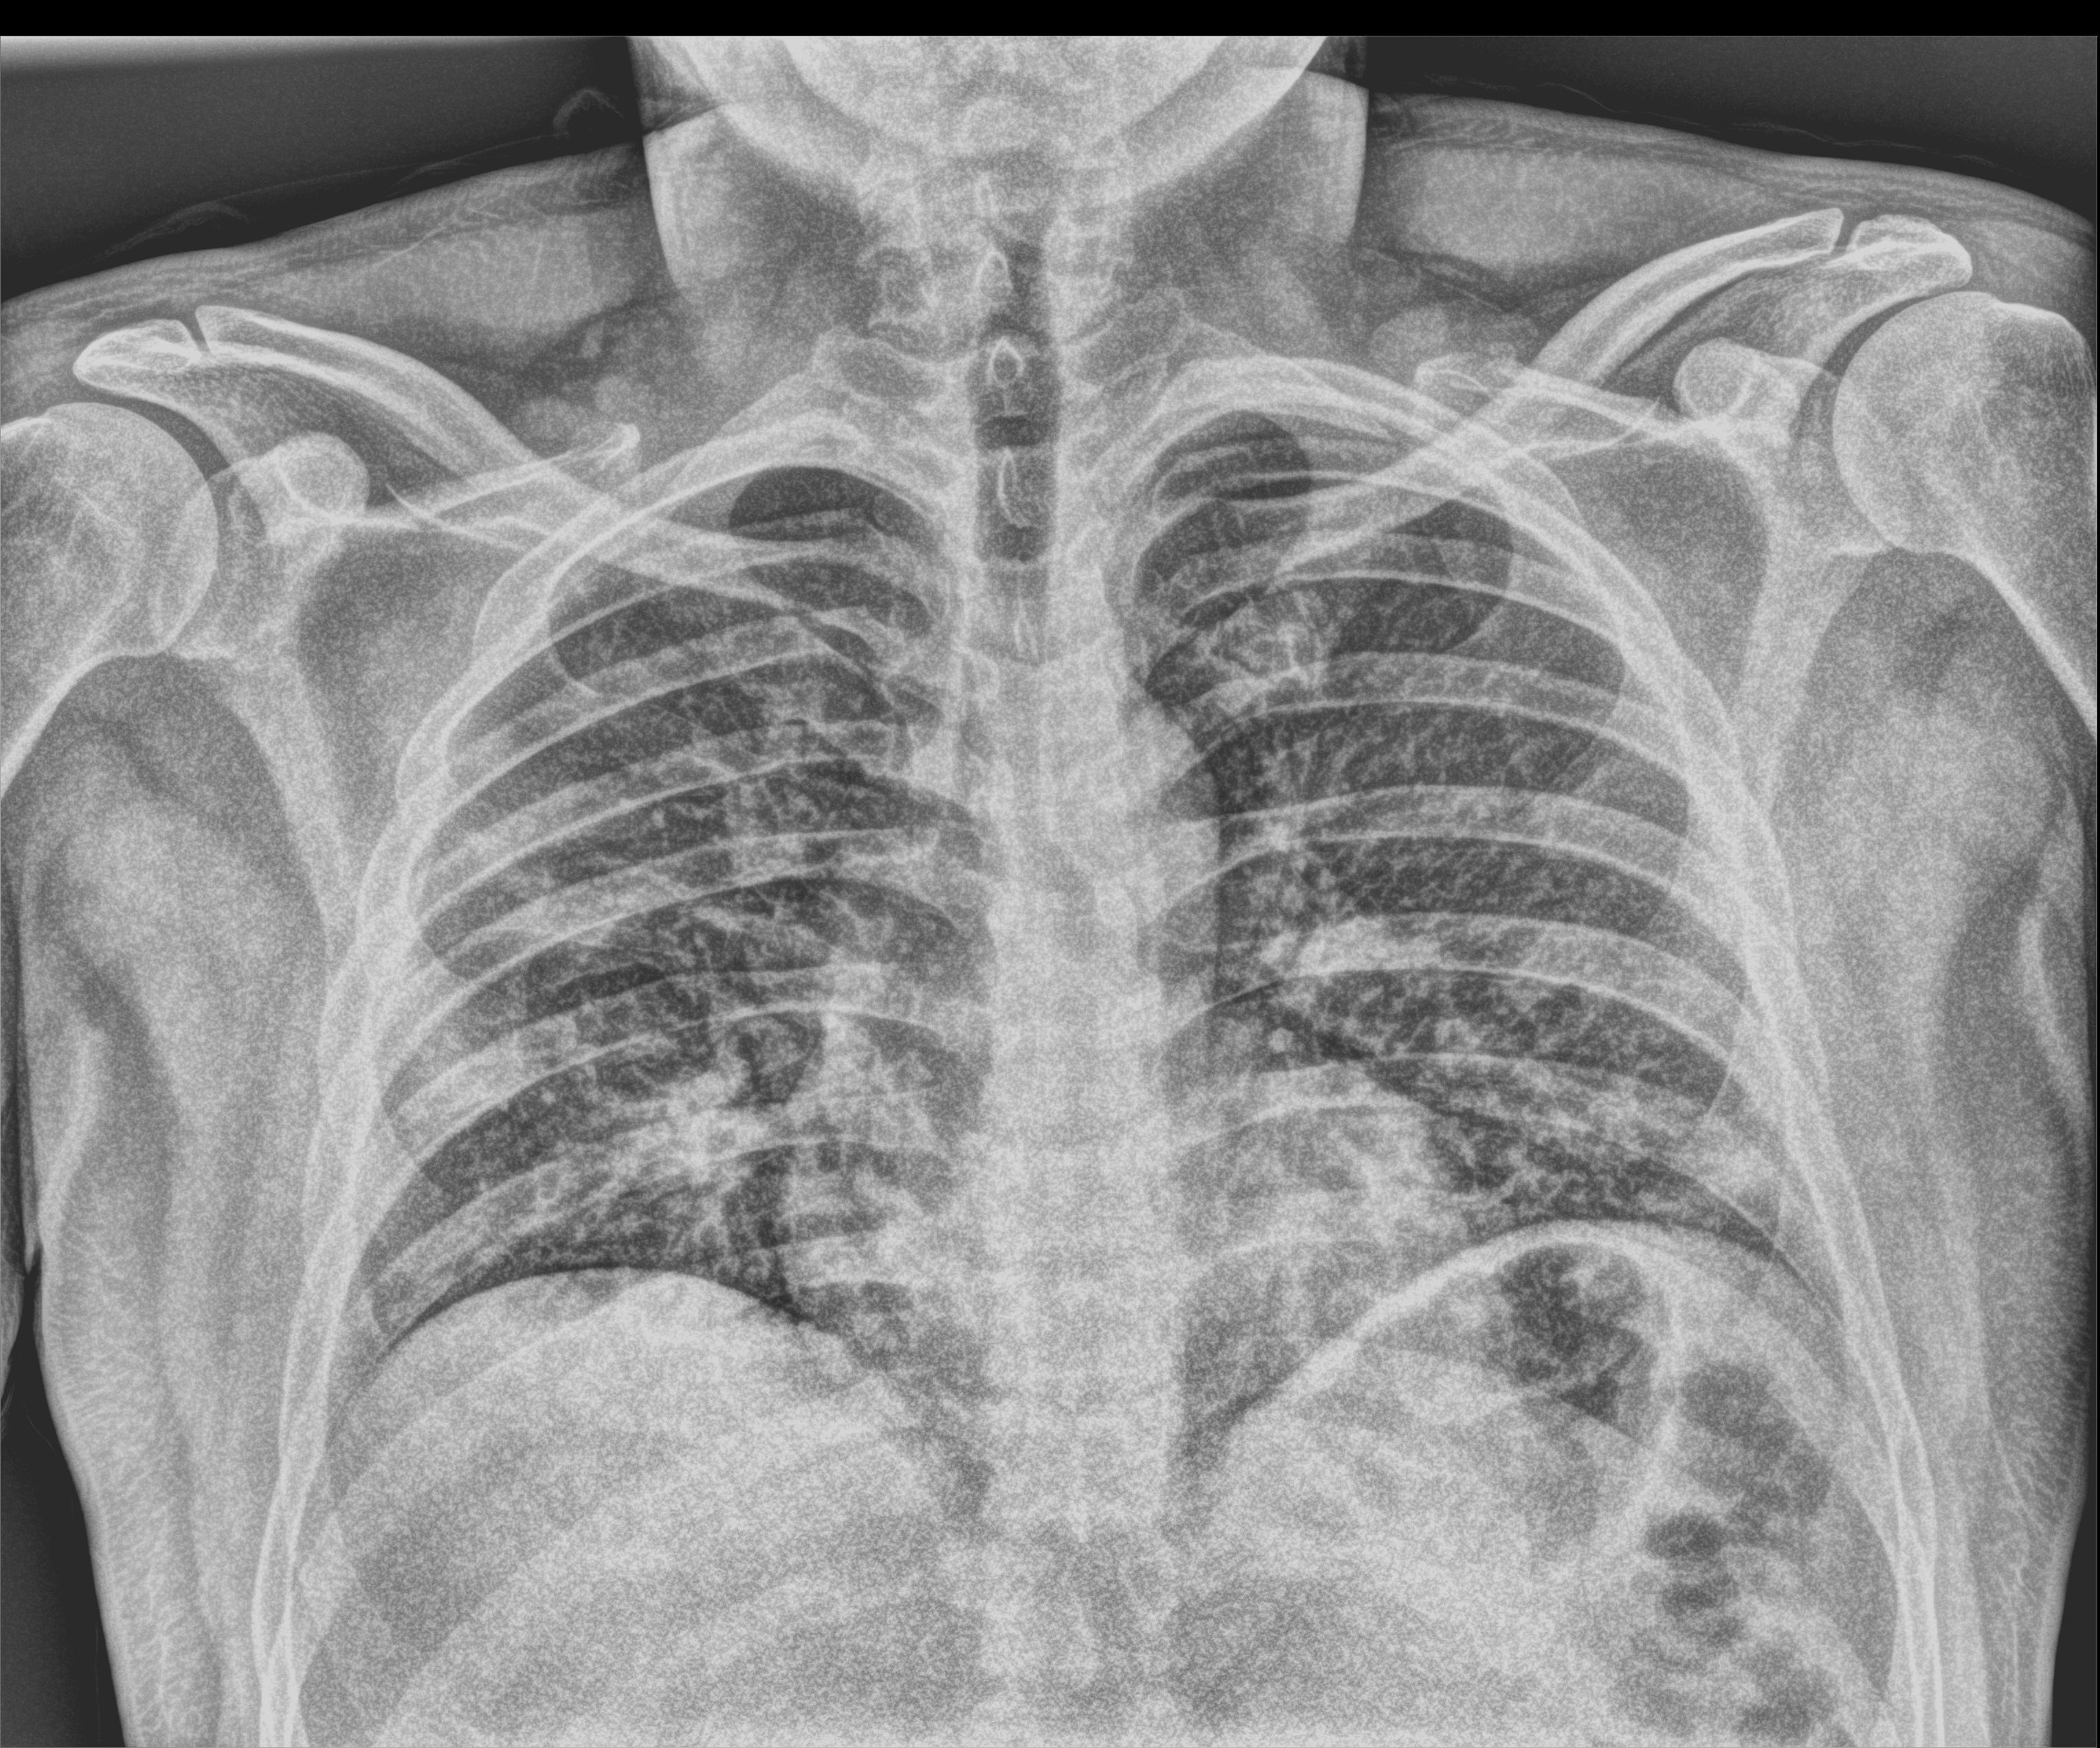
Bedside chest radiograph (computed radiography); anteroposterior (AP) projection. Patient hospitalised with COVID-19; male, aged 18–59 years.
Hospital-stay facts (about this admission, not read from this image; timing relative to this image not recorded):
- admitted to intensive care during this hospital stay: no
- length of hospital stay: 1 day
- other chronic lung disease (admission record): no